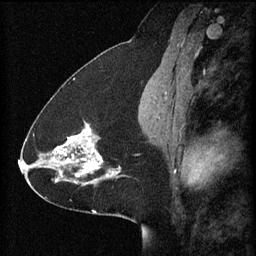
Breast MRI (dynamic contrast-enhanced), one sagittal slice; position 32 of 60 along the scan axis; 3 images stored at this slice position (order not interpretable as contrast timing); 1.5 T; TE 4.2 ms, TR 8.2 ms; 2 mm slice thickness; 256 × 256 image matrix, field of view 200 × 200 mm. Female patient, age 41 years.
Annotated regions visible in this slice (semi-automatically segmented with operator editing):
- analysis volume of interest (the breast-tissue region the enhancement analysis was run in; not a lesion): bounding box <58,120,122,181> (left, top, right, bottom; pixels)
- tumour enhancement mask (voxels above the 70 % enhancement threshold inside the analysis volume of interest): <58,124,122,181>